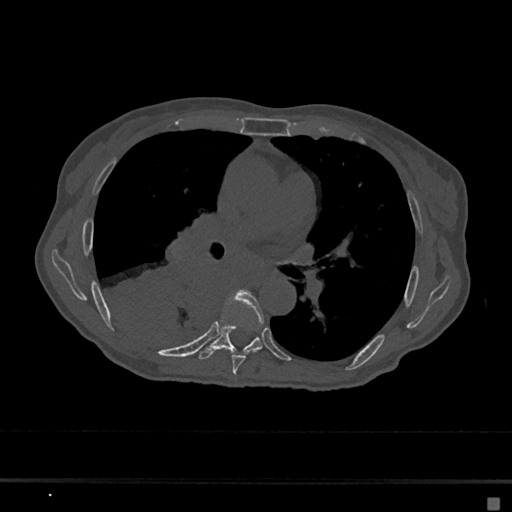
CT including the spine, one axial slice. Reconstruction kernel Br40s/3. Bone window (W 1800 / L 400 HU). 0.5 mm slice thickness. 512 × 512 image matrix, field of view 360 × 360 mm. Patient: female, 68 years. From the clinical record (not read from this slice): primary cancer: renal.
Outlined on this slice (semi-automatic segmentation, software-assisted and operator-edited):
- T6 vertebra: bounding box <230,290,264,375> (left, top, right, bottom; pixels)
- T7 vertebra: <199,325,263,360>